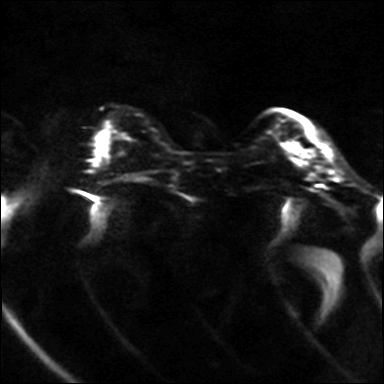
Breast MRI, one axial slice; position 8 of 36 along the scan axis; diffusion-weighted series; image 2 of 4 stored at this slice position (different b-values; order by instance number); 3 T; 384 × 384 image matrix, field of view 320 × 320 mm. Female patient.
Annotated regions visible in this slice (expert manual segmentation):
- tumour on diffusion-weighted imaging: bounding box <293,146,299,152> (left, top, right, bottom; pixels)